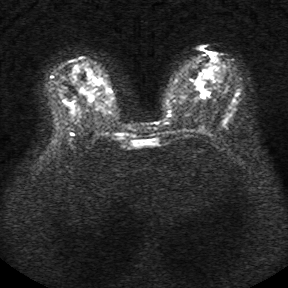
Breast MRI, one axial slice. Slice 17 of 34 in the series (ordered by position). Diffusion-weighted series; image 2 of 4 stored at this slice position (different b-values; order by instance number). 1.5 T. 5 mm slice thickness. 288 × 288 image matrix. Female patient.
Annotated regions visible in this slice (manually delineated by an expert):
- tumour on diffusion-weighted imaging: bounding box <201,95,204,98> (left, top, right, bottom; pixels)